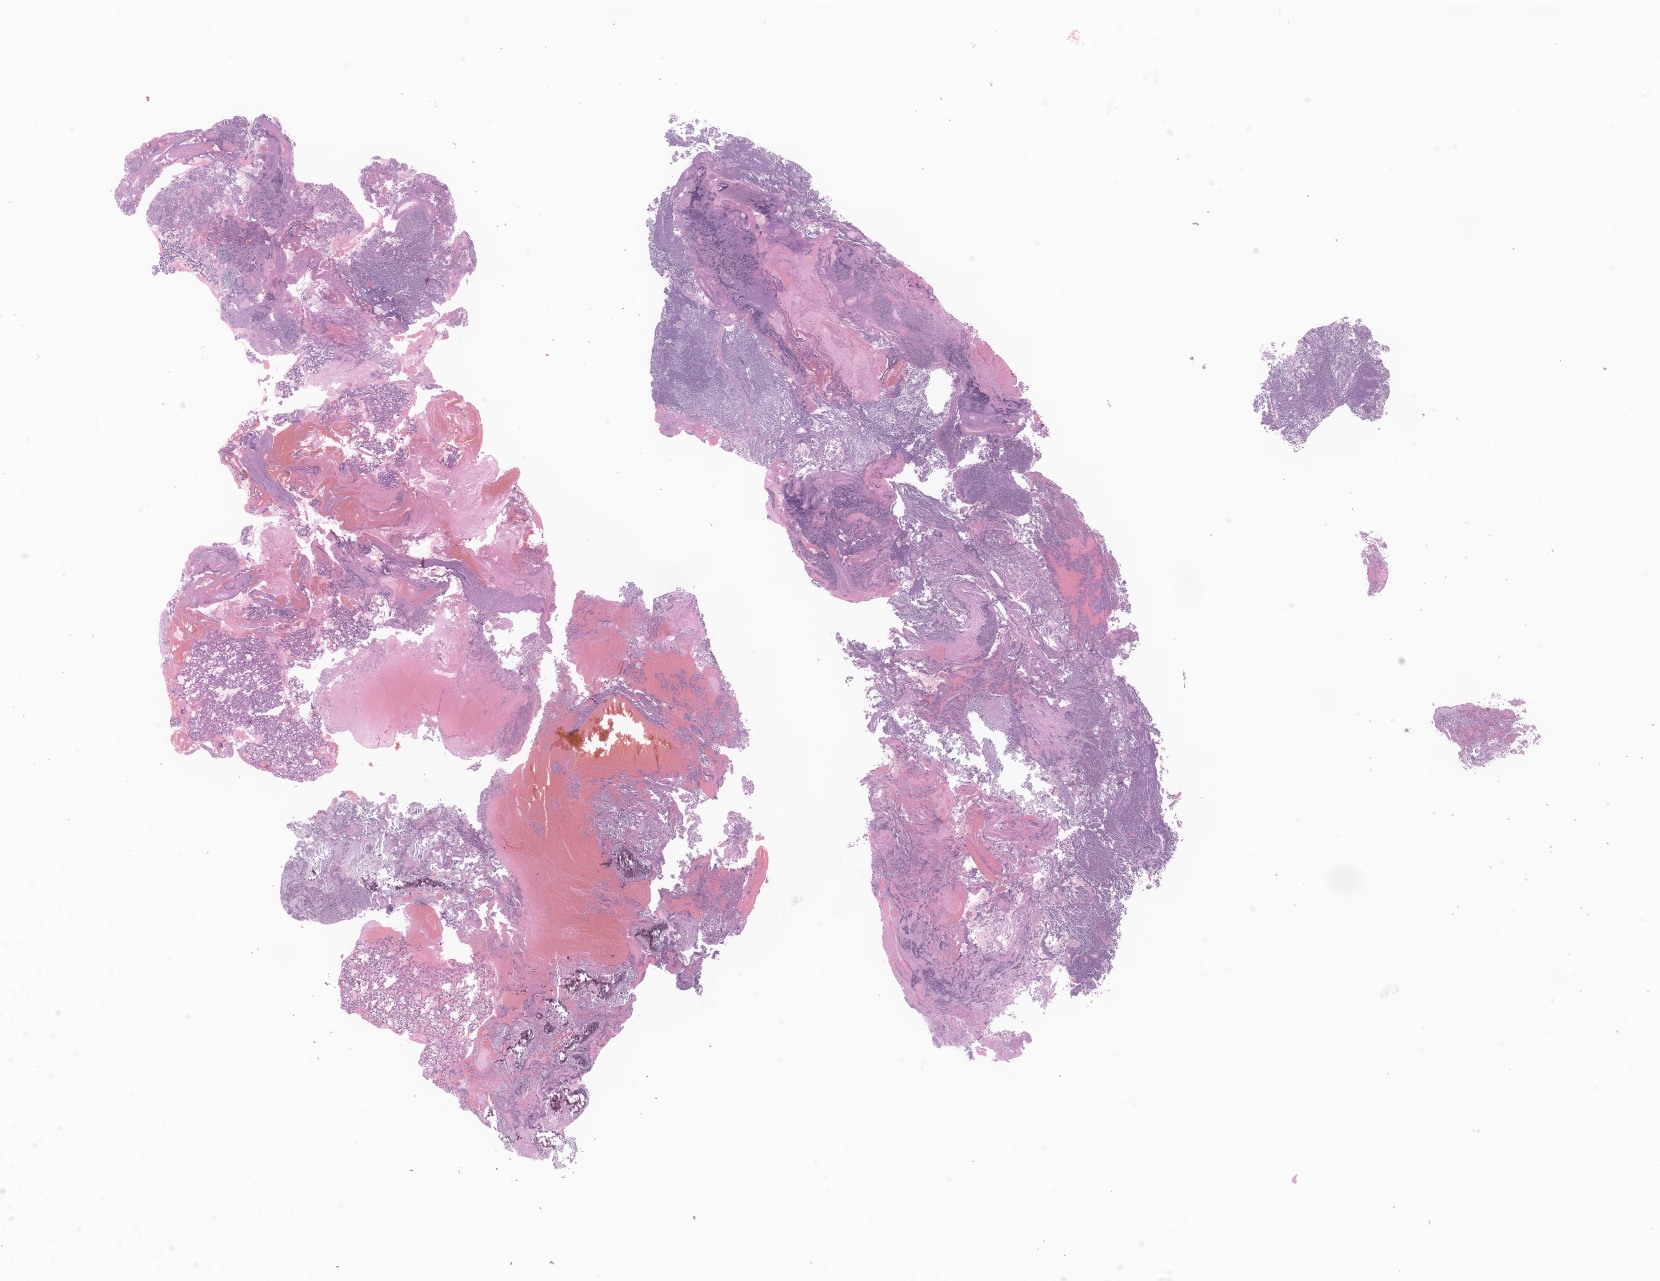
Whole-slide image, haematoxylin and eosin stain of tumor tissue from the brain — low-resolution overview of the scanned area, about 28.0 x 21.6 mm, formalin-fixed paraffin-embedded section. Male patient, age 57 months (4 years 9 months).
Diagnosis (ICD-O-3 morphology term): Medulloblastoma, NOS.